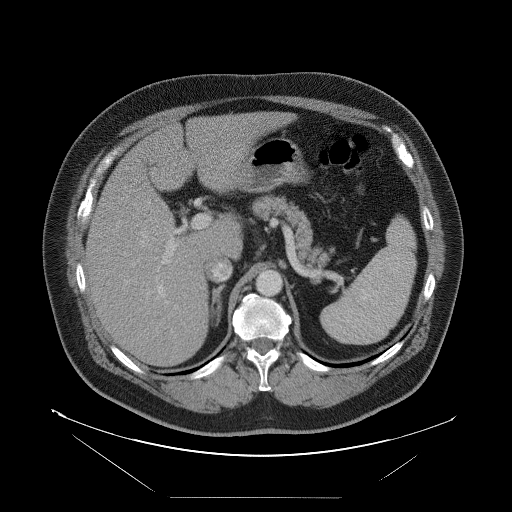
Contrast-enhanced abdominal CT, one axial slice. Position 60 of 114 along the scan axis. 120 kVp. Intravenous contrast given. Soft-tissue window (W 400 / L 40 HU). 5 mm slice thickness. 512 × 512 image matrix, field of view 500 × 500 mm. Male patient, age 61 years. Case-level facts recorded for this patient, not image findings: diagnosis: colorectal cancer liver metastases, imaged before liver resection; multiple liver metastases: no.
Structures marked on this image (manually delineated by an expert):
- hepatic veins: bounding box [x1, y1, x2, y2] px = [140, 231, 153, 246]
- liver: [87, 112, 285, 366]
- planned liver remnant (the part of the liver to remain after resection): [145, 112, 284, 249]
- portal vein (with intrahepatic branches): [156, 215, 210, 302]